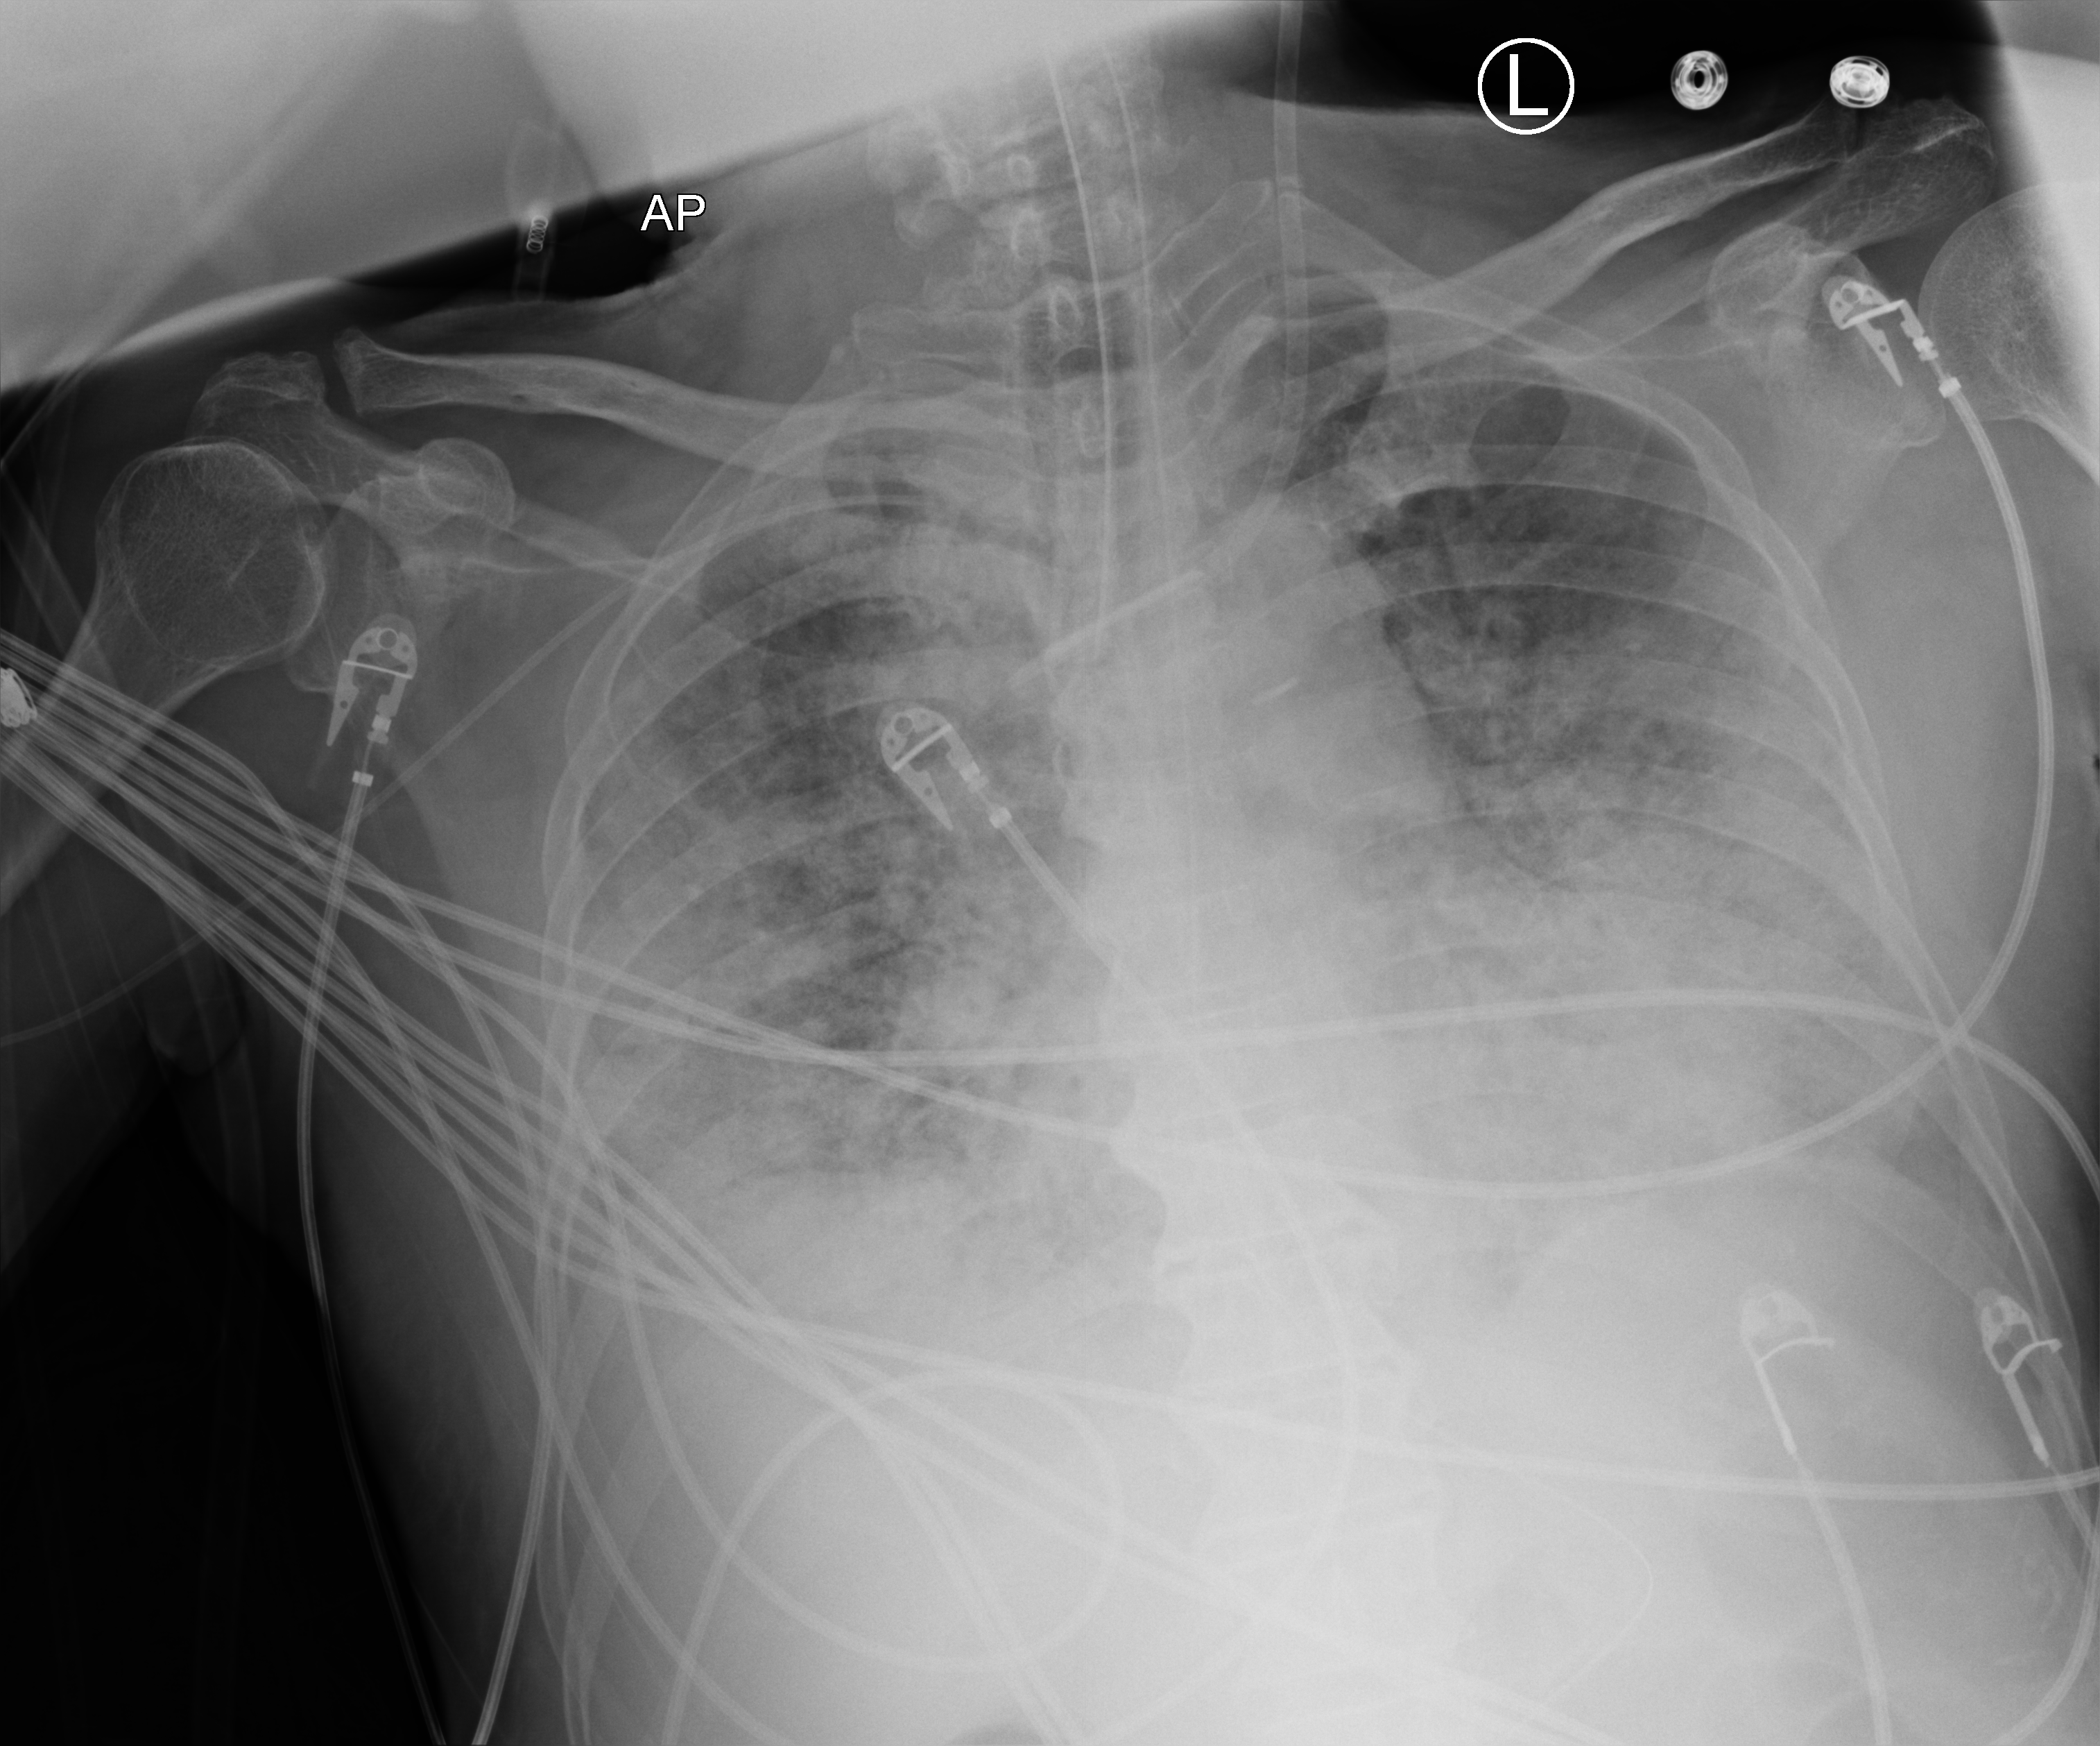
Bedside chest radiograph (computed radiography), anteroposterior (AP) projection. Male patient hospitalised with COVID-19, age 60–74 years.
Admission-level facts for this patient (not findings on this image; timing relative to this image not recorded):
- chronic kidney disease (admission record): no
- length of hospital stay: 26 days
- admitted to intensive care during this hospital stay: yes